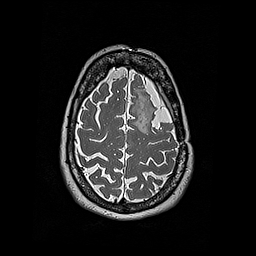
Brain MRI from a brain-tumour surgery series, one axial slice; slice 143 of 192 in the series (ordered by position); 1 mm slice thickness; 256 × 256 image matrix. Case-level facts recorded for this patient, not image findings: histopathology: Oligodendroglioma; WHO grade: 2; IDH mutation: yes; tumour location: Left Frontal.
Outlined on this slice (outlined manually by an expert reader):
- tumour: box from (x=145, y=112) to (x=153, y=130) px